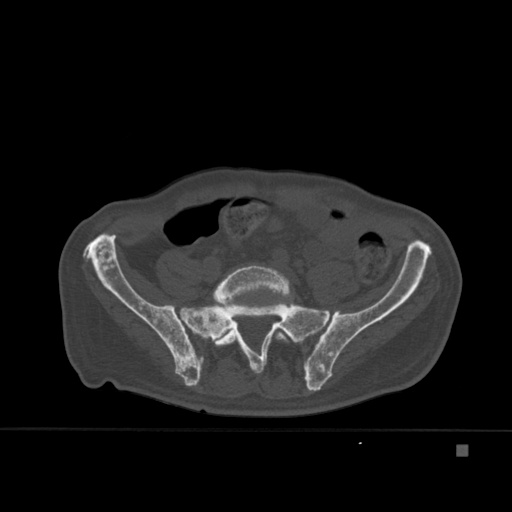
CT including the spine, one axial slice; slice 94 of 451 in the series (ordered by position); bone window (W 1800 / L 400 HU); 1.5 mm slice thickness; 512 × 512 image matrix, field of view 378 × 378 mm. Patient: male, 75 years. From the clinical record (not read from this slice): primary cancer: prostate.
Structures marked on this image (semi-automatically segmented with operator editing):
- L5 vertebra: bounding box <213,265,290,363> (left, top, right, bottom; pixels)